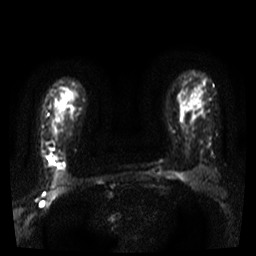
Breast MRI, one axial slice. Slice 28 of 36 in the series (ordered by position). Diffusion-weighted series; image 2 of 4 stored at this slice position (different b-values; order by instance number). 3 T. 256 × 256 image matrix, field of view 300 × 300 mm. Female patient.
Structures marked on this image (manually delineated by an expert):
- tumour on diffusion-weighted imaging: bounding box [x1, y1, x2, y2] px = [48, 156, 53, 162]